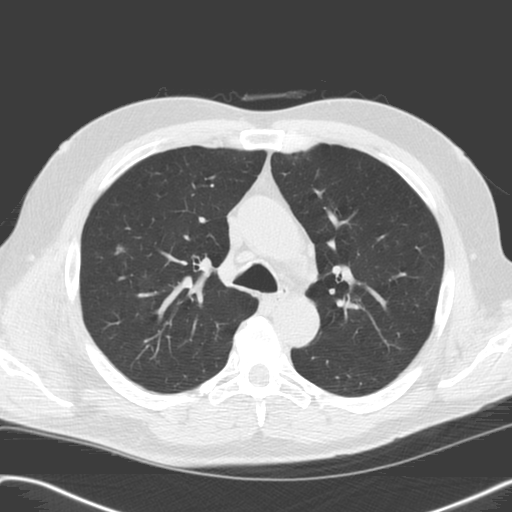
Chest CT (low-dose screening protocol), one axial image; baseline annual screen; lung window (W 1500 / L -600 HU); 3.2 mm slice thickness; standard (soft-tissue) reconstruction kernel (C). Male participant, aged 61 years at enrolment.
Expert-annotated lung lesion, box from (x=105, y=230) to (x=136, y=270) px. Screening reader's record for this exam (one nodule recorded; not confirmed to be the boxed lesion): non-calcified nodule or mass ≥4 mm, right upper lobe, 6 × 6 mm, smooth margins, soft tissue attenuation. Official screen result: positive, change unspecified: nodule(s) >= 4 mm or enlarging nodule(s), mass(es), or other non-specific abnormalities suspicious for lung cancer. Later outcome: lung cancer diagnosed 746 days after this screen — adenocarcinoma, NOS, right upper lobe, stage IIIA (AJCC 6th edition), 13 mm at pathology.